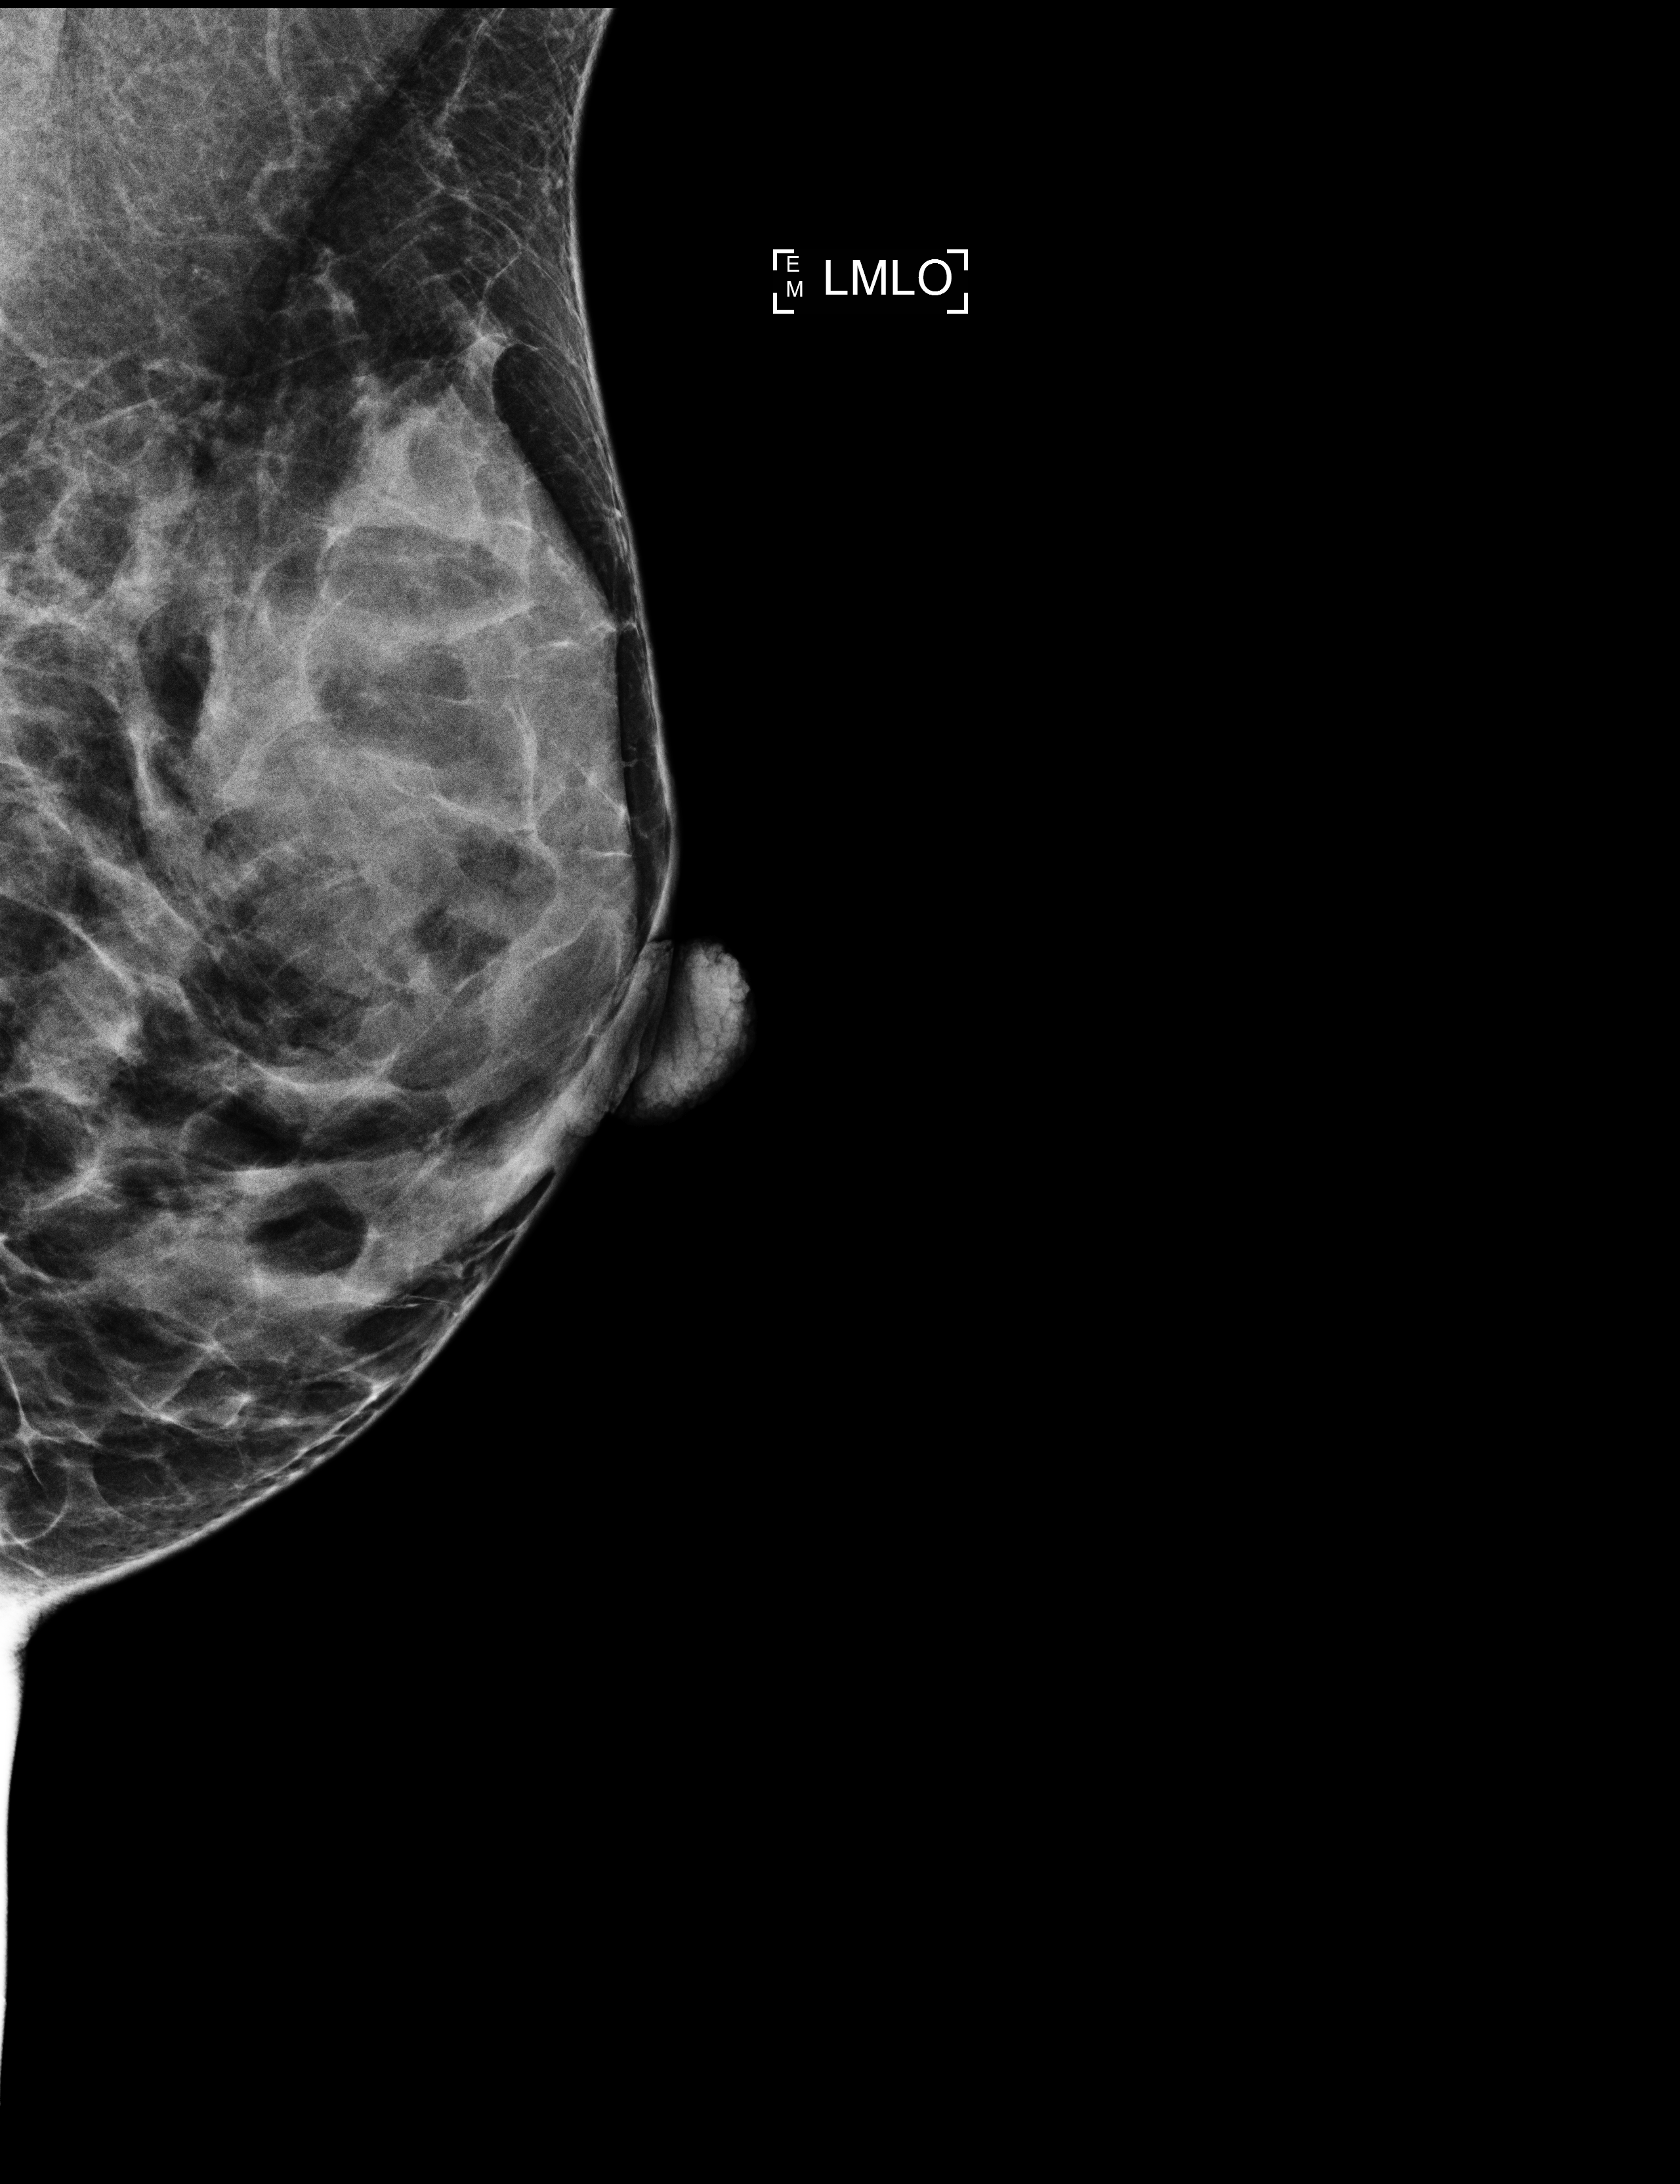
Annual screening mammography examination; compressed breast thickness 31 mm; system: Selenia Dimensions. Patient aged 43 years (female).
Image type: full-field digital mammogram. Breast: left. Projection: MLO view.